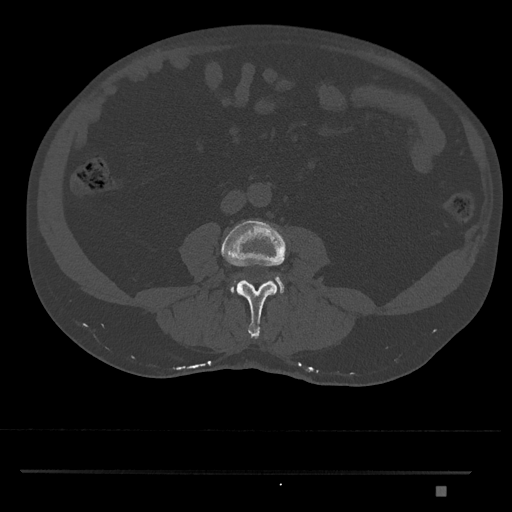
CT including the spine, one axial slice. Position 662 of 1134 along the scan axis. Reconstruction kernel Br40s/3. 120 kVp. Bone window (W 1800 / L 400 HU). 0.5 mm slice thickness. 512 × 512 image matrix, field of view 429 × 429 mm. Patient: male, 65 years. From the clinical record (not read from this slice): primary cancer: prostate.
Outlined on this slice (semi-automatically segmented with operator editing):
- L3 vertebra: box from (x=221, y=220) to (x=287, y=339) px
- L4 vertebra: (x=230, y=275)–(x=284, y=294)